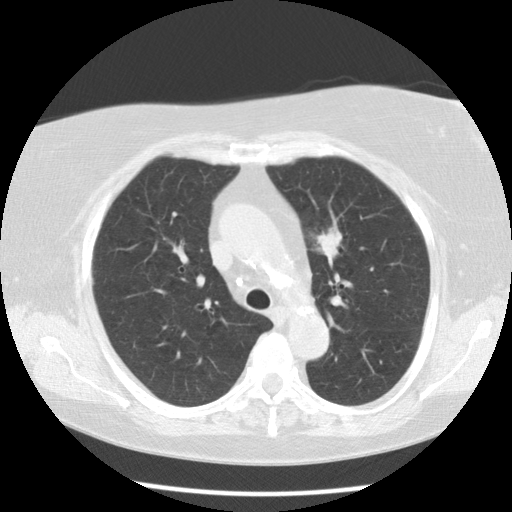
Axial slice from a low-dose chest CT screening exam; second screening round (one year after baseline); lung window (W 1500 / L -600 HU); 2.5 mm slice thickness; standard (soft-tissue) reconstruction kernel (STANDARD); slice 29 of 109 in the series; 512 × 512 image matrix, field of view 334 × 334 mm. Female, age 67 years at enrolment. Former smoker at enrolment.
Expert reader's lesion annotation, bounding box (x1, y1, x2, y2) in pixels: (292, 214, 353, 270). Screening reader's record for this exam (one nodule recorded; not confirmed to be the boxed lesion): non-calcified nodule or mass ≥4 mm, left upper lobe, 20 × 18 mm, poorly defined margins, soft tissue attenuation, pre-existing on the prior screen: yes; interval growth: yes.